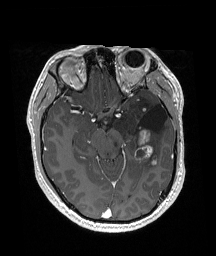
Brain MRI from a brain-tumour surgery series, one axial slice; position 107 of 192 along the scan axis; T1-weighted post-contrast; 1 mm slice thickness; 216 × 256 image matrix. From the clinical record (not read from this slice): histopathology: Glioneuronal tumor; WHO grade: 2.
Annotated regions visible in this slice (manually delineated by an expert):
- previous resection cavity: bounding box <139,104,168,132> (left, top, right, bottom; pixels)
- tumour: <134,107,159,164>